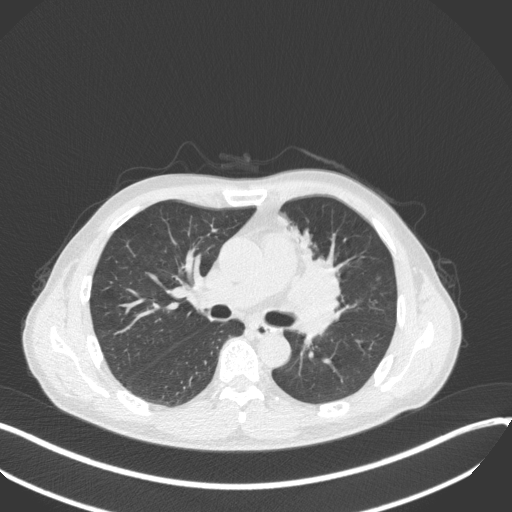
Chest CT, one axial slice; slice 198 of 411 in the series (ordered by position); reconstruction kernel B31f; 120 kVp; lung window (W 1500 / L -600 HU); 1 mm slice thickness; 512 × 512 image matrix, field of view 400 × 400 mm. Male patient, age 56 years. From the clinical record (not read from this slice): clinical TNM (as recorded): T2a N0 M0.
Outlined on this slice (bounding box drawn by a radiologist):
- lung tumour (recorded histology: squamous cell carcinoma): bounding box <278,218,345,310> (left, top, right, bottom; pixels)